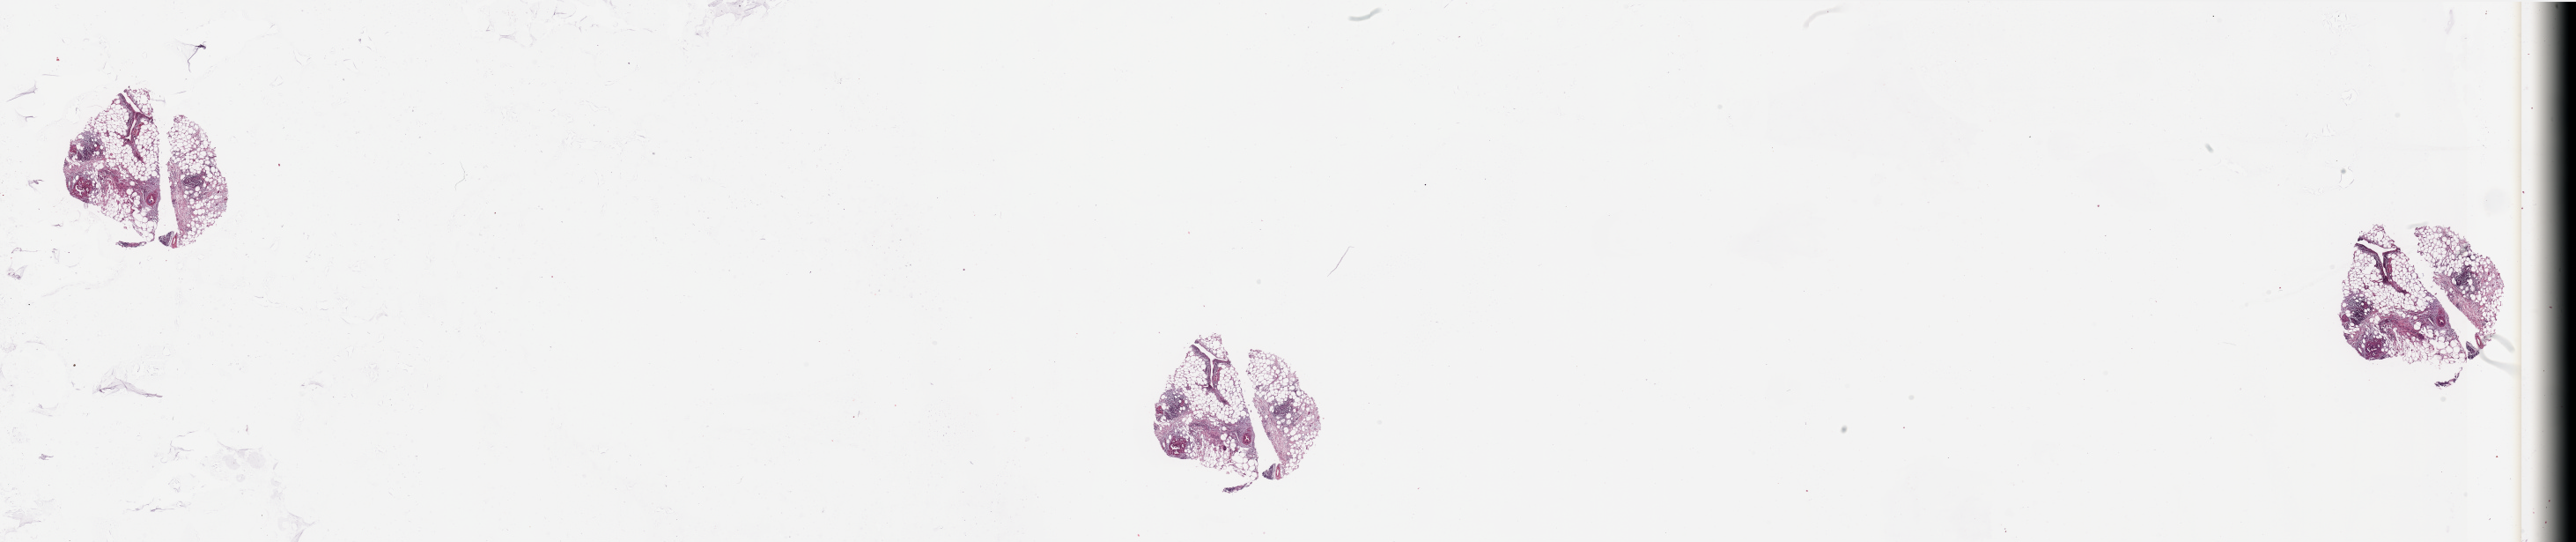
H&E-stained whole-slide image — low-resolution overview of the scanned area, about 46.3 x 9.7 mm, tumour tissue sample, pancreas. Patient: female, age 70 years.
Patient diagnosis (cohort enrolment): ductal adenocarcinoma (pancreas).